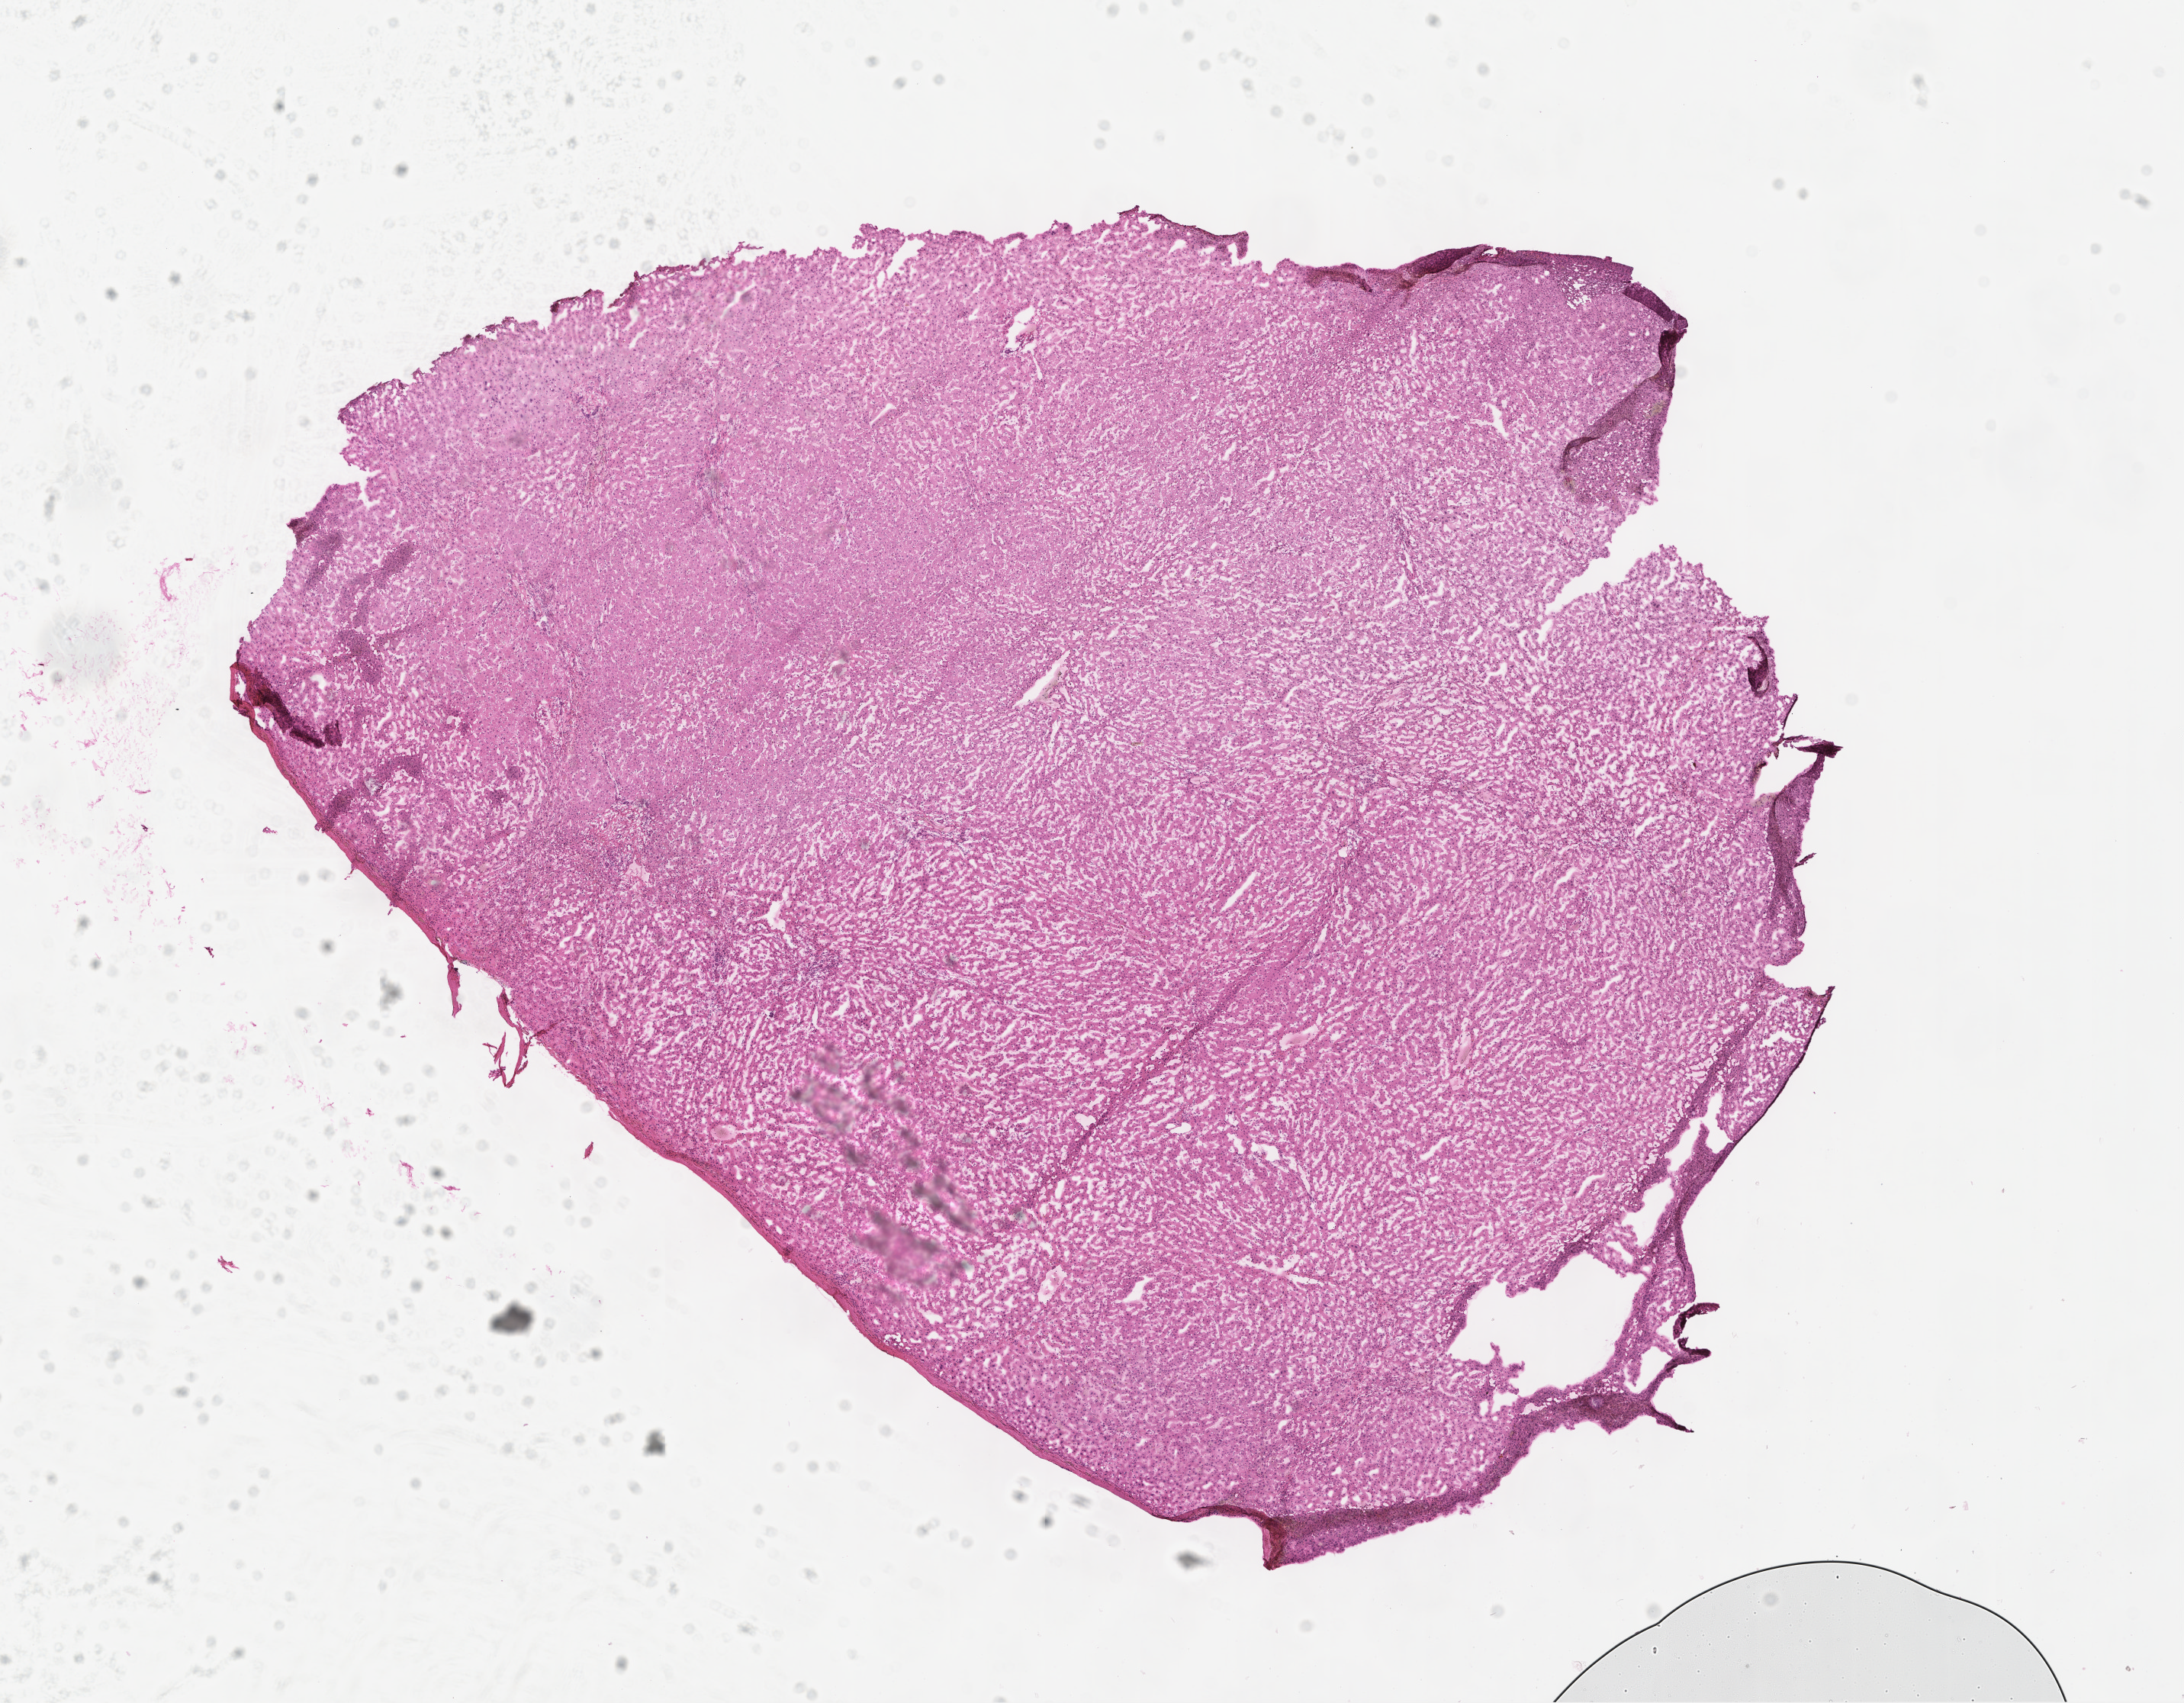
Whole-slide image, hematoxylin and eosin (H&E) stain, shown as a low-resolution overview of the whole scanned area (about 11.6 x 9.0 mm), frozen section (tissue freezing medium), normal-tissue sample (non-tumor) from a patient with adenocarcinoma, NOS, site: rectum. Male, age 71 years at initial diagnosis. Pathologist review of this section (percent, as recorded): tumor cells 0%, tumor nuclei 0%, stromal cells 0%, necrosis 0%, normal cells 100%. Inflammatory infiltration, as recorded: lymphocyte infiltration 5%, monocyte infiltration 2%, neutrophil infiltration 0%.
This section: non-tumor tissue sample; the patient's diagnosis is given above. Section: top of the tissue portion.